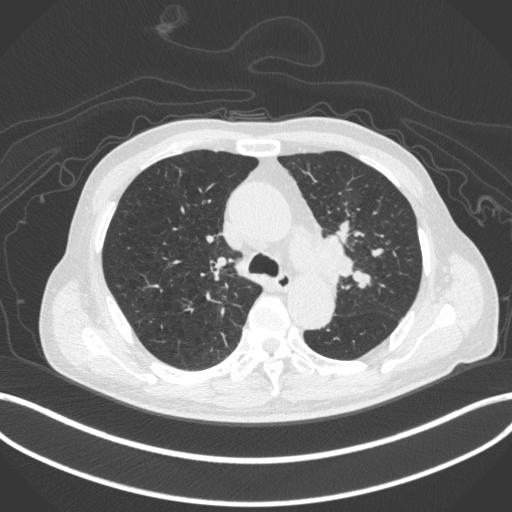
Chest CT, one axial slice; position 296 of 420 along the scan axis; reconstruction kernel B31f; 120 kVp; lung window (W 1500 / L -600 HU); 1 mm slice thickness; 512 × 512 image matrix, field of view 400 × 400 mm. Male patient, age 77 years. Case-level facts recorded for this patient, not image findings: clinical TNM (as recorded): T3 N1 M0.
Structures marked on this image (bounding box drawn by a radiologist):
- lung tumour (recorded histology: adenocarcinoma): box from (x=308, y=229) to (x=356, y=282) px